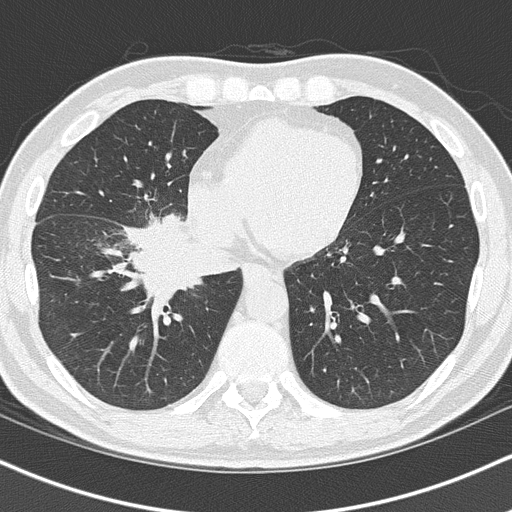
Chest CT (low-dose screening protocol), one axial image; baseline screening round; lung window (W 1500 / L -600 HU); 2 mm slice thickness; 120 kVp. Male, age 55 years at enrolment. Current smoker at enrolment.
Lesion marked by an expert reader, box from (x=125, y=224) to (x=242, y=313) px. Reader record for this screening exam (exam-level; its link to the box is not recorded): non-calcified nodule or mass ≥4 mm, right lower lobe, 6 × 5 mm, spiculated (stellate) margins, soft tissue attenuation. Later outcome: lung cancer diagnosed 21 days after this screen — carcinoma, NOS, right hilum, stage IB (AJCC 6th edition), 67 mm at pathology.